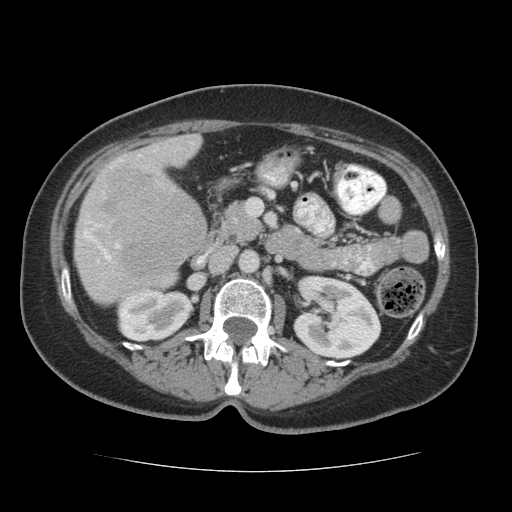
Contrast-enhanced abdominal CT (liver protocol), one axial slice. Position 20 of 75 along the scan axis. Reconstruction kernel STANDARD. 140 kVp. Soft-tissue window (W 400 / L 40 HU). 2.5 mm slice thickness. 512 × 512 image matrix, field of view 360 × 360 mm. Case-level facts recorded for this patient, not image findings: diagnosis: hepatocellular carcinoma (patient treated with transarterial chemoembolisation; whether this scan precedes or follows treatment is not stated here); TNM stage (as recorded): Stage-I; Child-Pugh class: A.
Outlined on this slice (semi-automatically segmented with operator editing):
- liver parenchyma outside the tumour (the mass and vessels are separate outlines, so this box may not span the whole liver): bounding box (x1, y1, x2, y2) in pixels: (74, 134, 206, 304)
- mass: (93, 161, 204, 283)
- liver vessels: (82, 142, 193, 263)